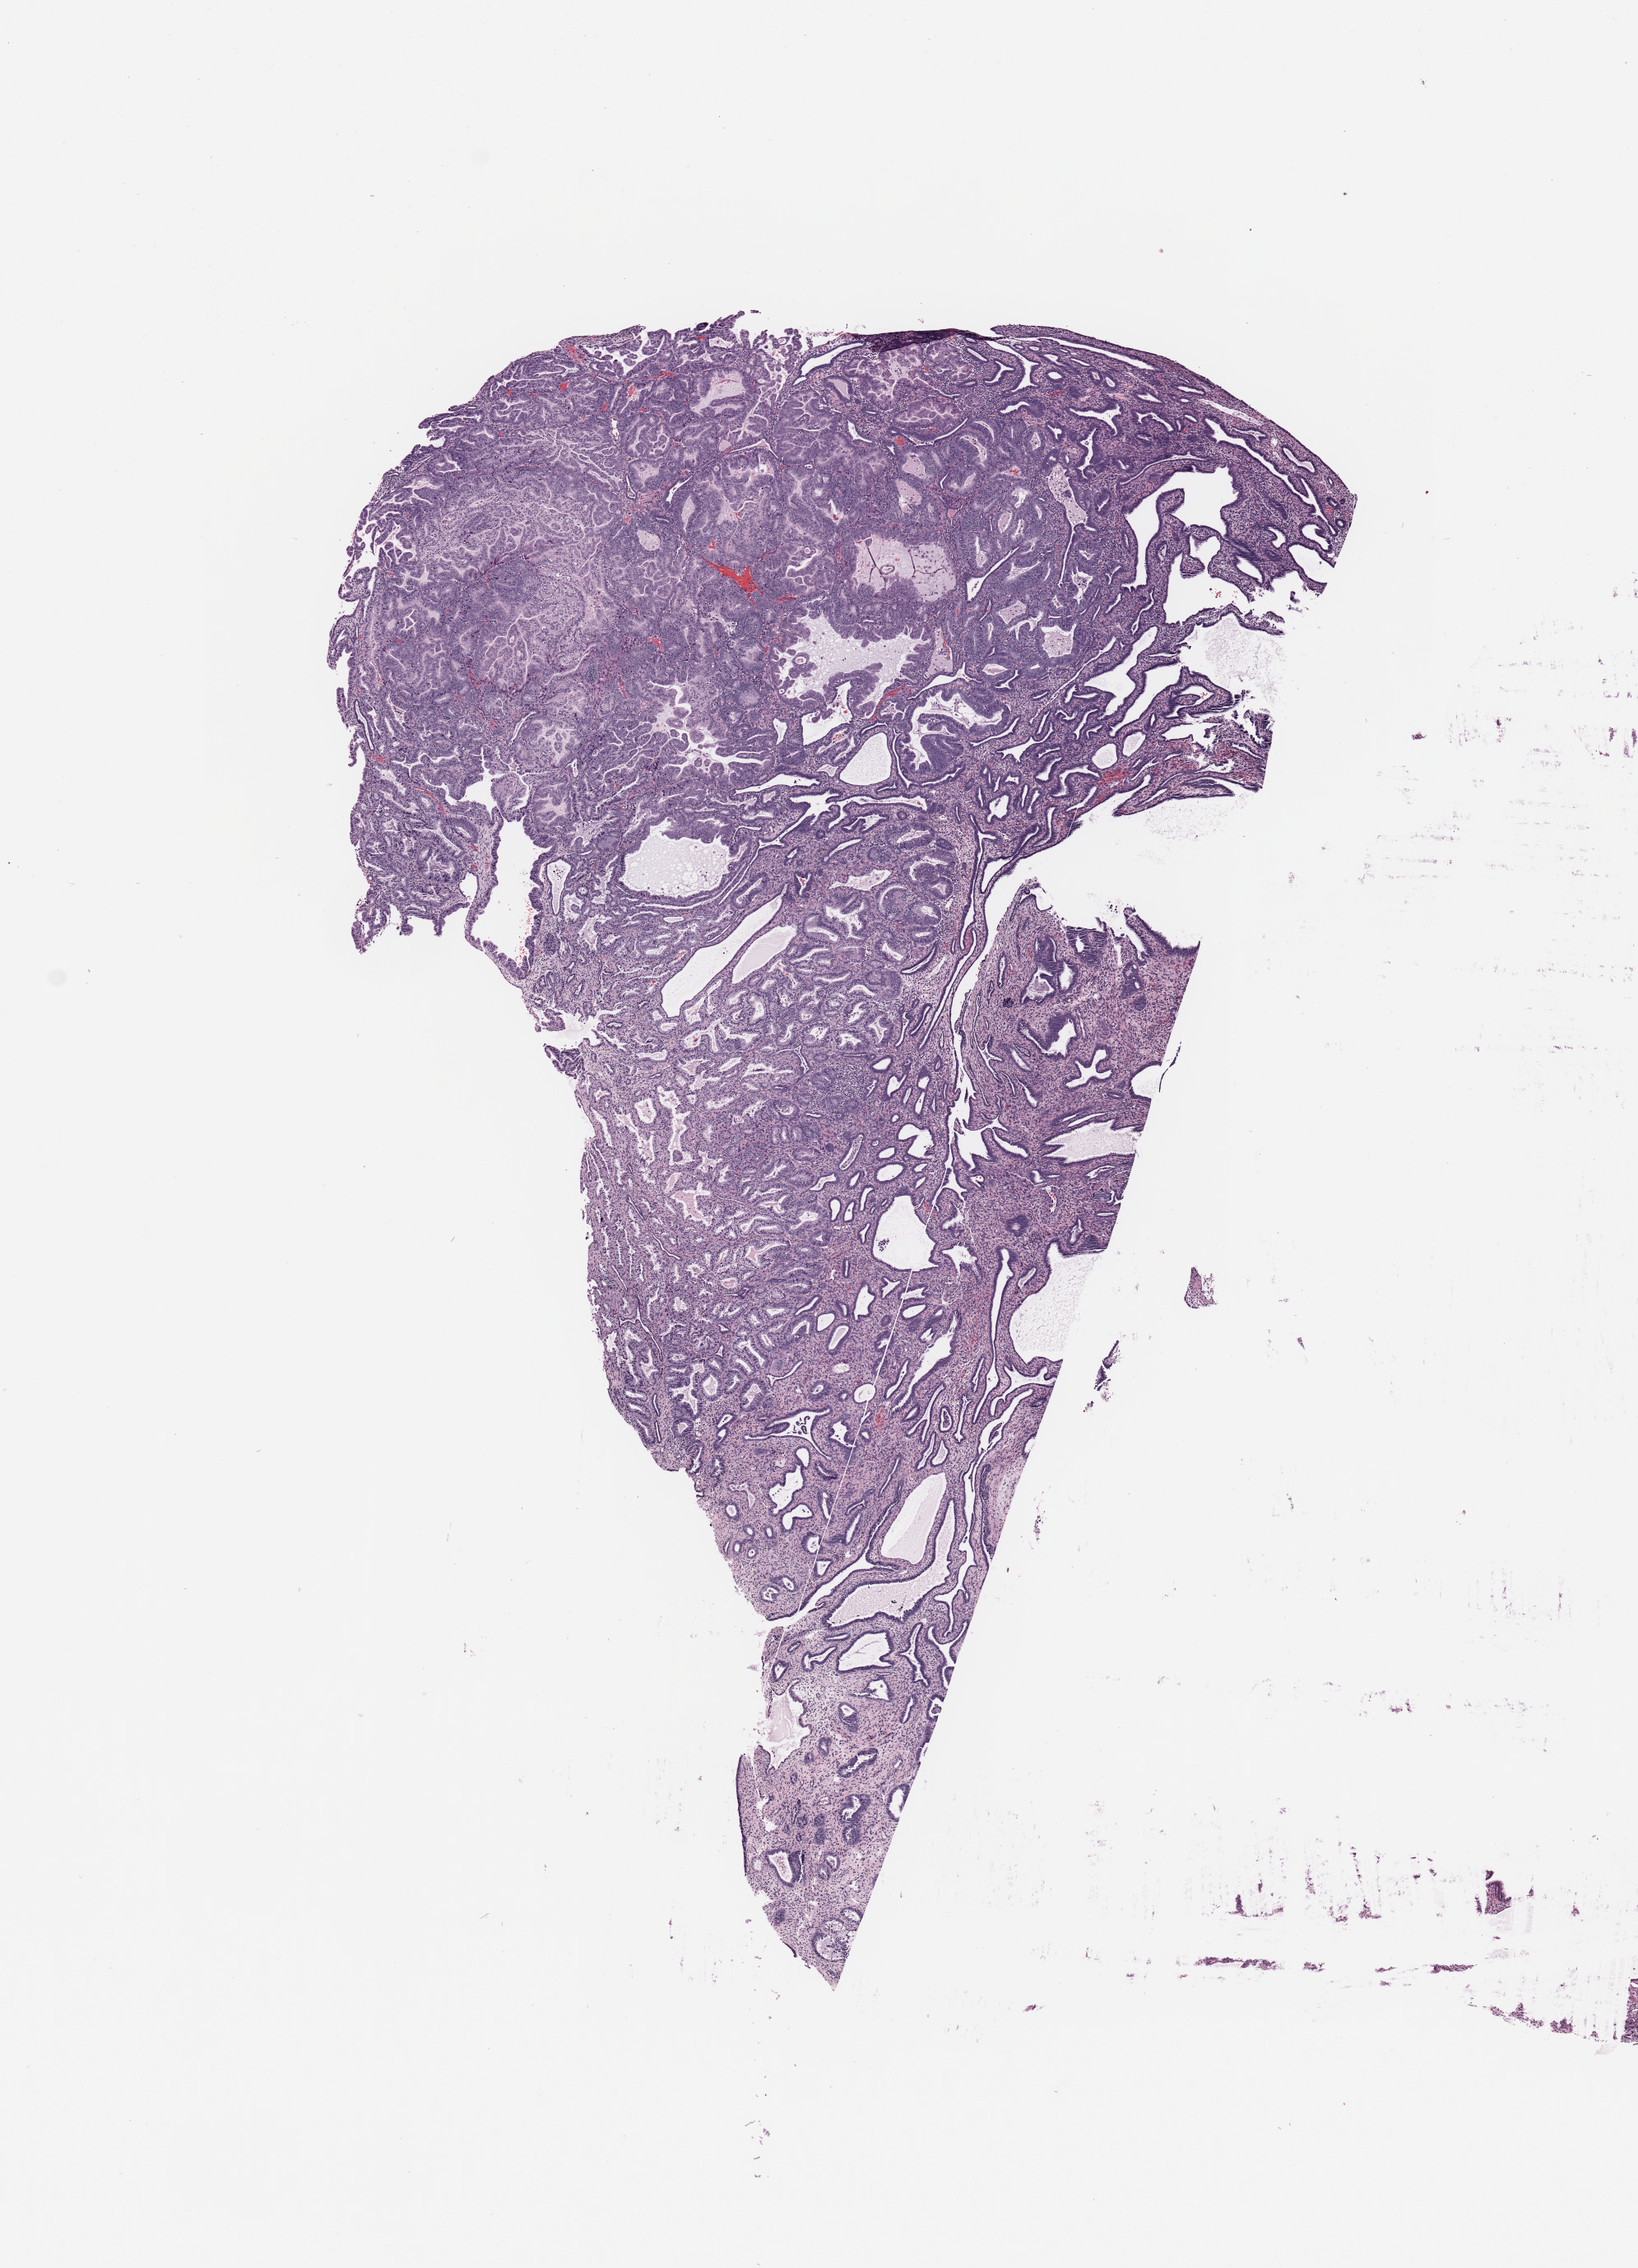
Digitized Hematoxylin and eosin (H&E) stained tissue section (whole slide), shown as a low-resolution overview of the whole scanned area (about 7.9 x 10.9 mm, from a 20x scan); tumour tissue sample, sampled site: uterus. 76-year-old female patient. Histologic grade: G1 (well differentiated). Slide review estimates, as recorded: tumour nuclei 95%, necrosis 0%.
Histologic diagnosis: Endometrioid adenocarcinoma, NOS. AJCC pathologic stage: I. Primary tumour site (as recorded): posterior endometrium.